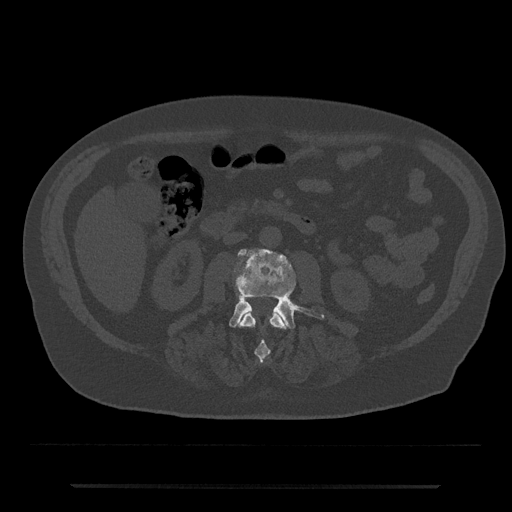
CT including the spine, one axial slice; position 432 of 797 along the scan axis; 120 kVp; bone window (W 1800 / L 400 HU); 0.5 mm slice thickness; 512 × 512 image matrix, field of view 434 × 434 mm. Male patient, age 80 years. Case-level facts recorded for this patient, not image findings: primary cancer: prostate; vertebrae with lytic lesions (as recorded): L1, T11.
Annotated regions visible in this slice (semi-automatic segmentation, software-assisted and operator-edited):
- L2 vertebra: box from (x=240, y=310) to (x=286, y=362) px
- L3 vertebra: (x=229, y=249)–(x=324, y=329)